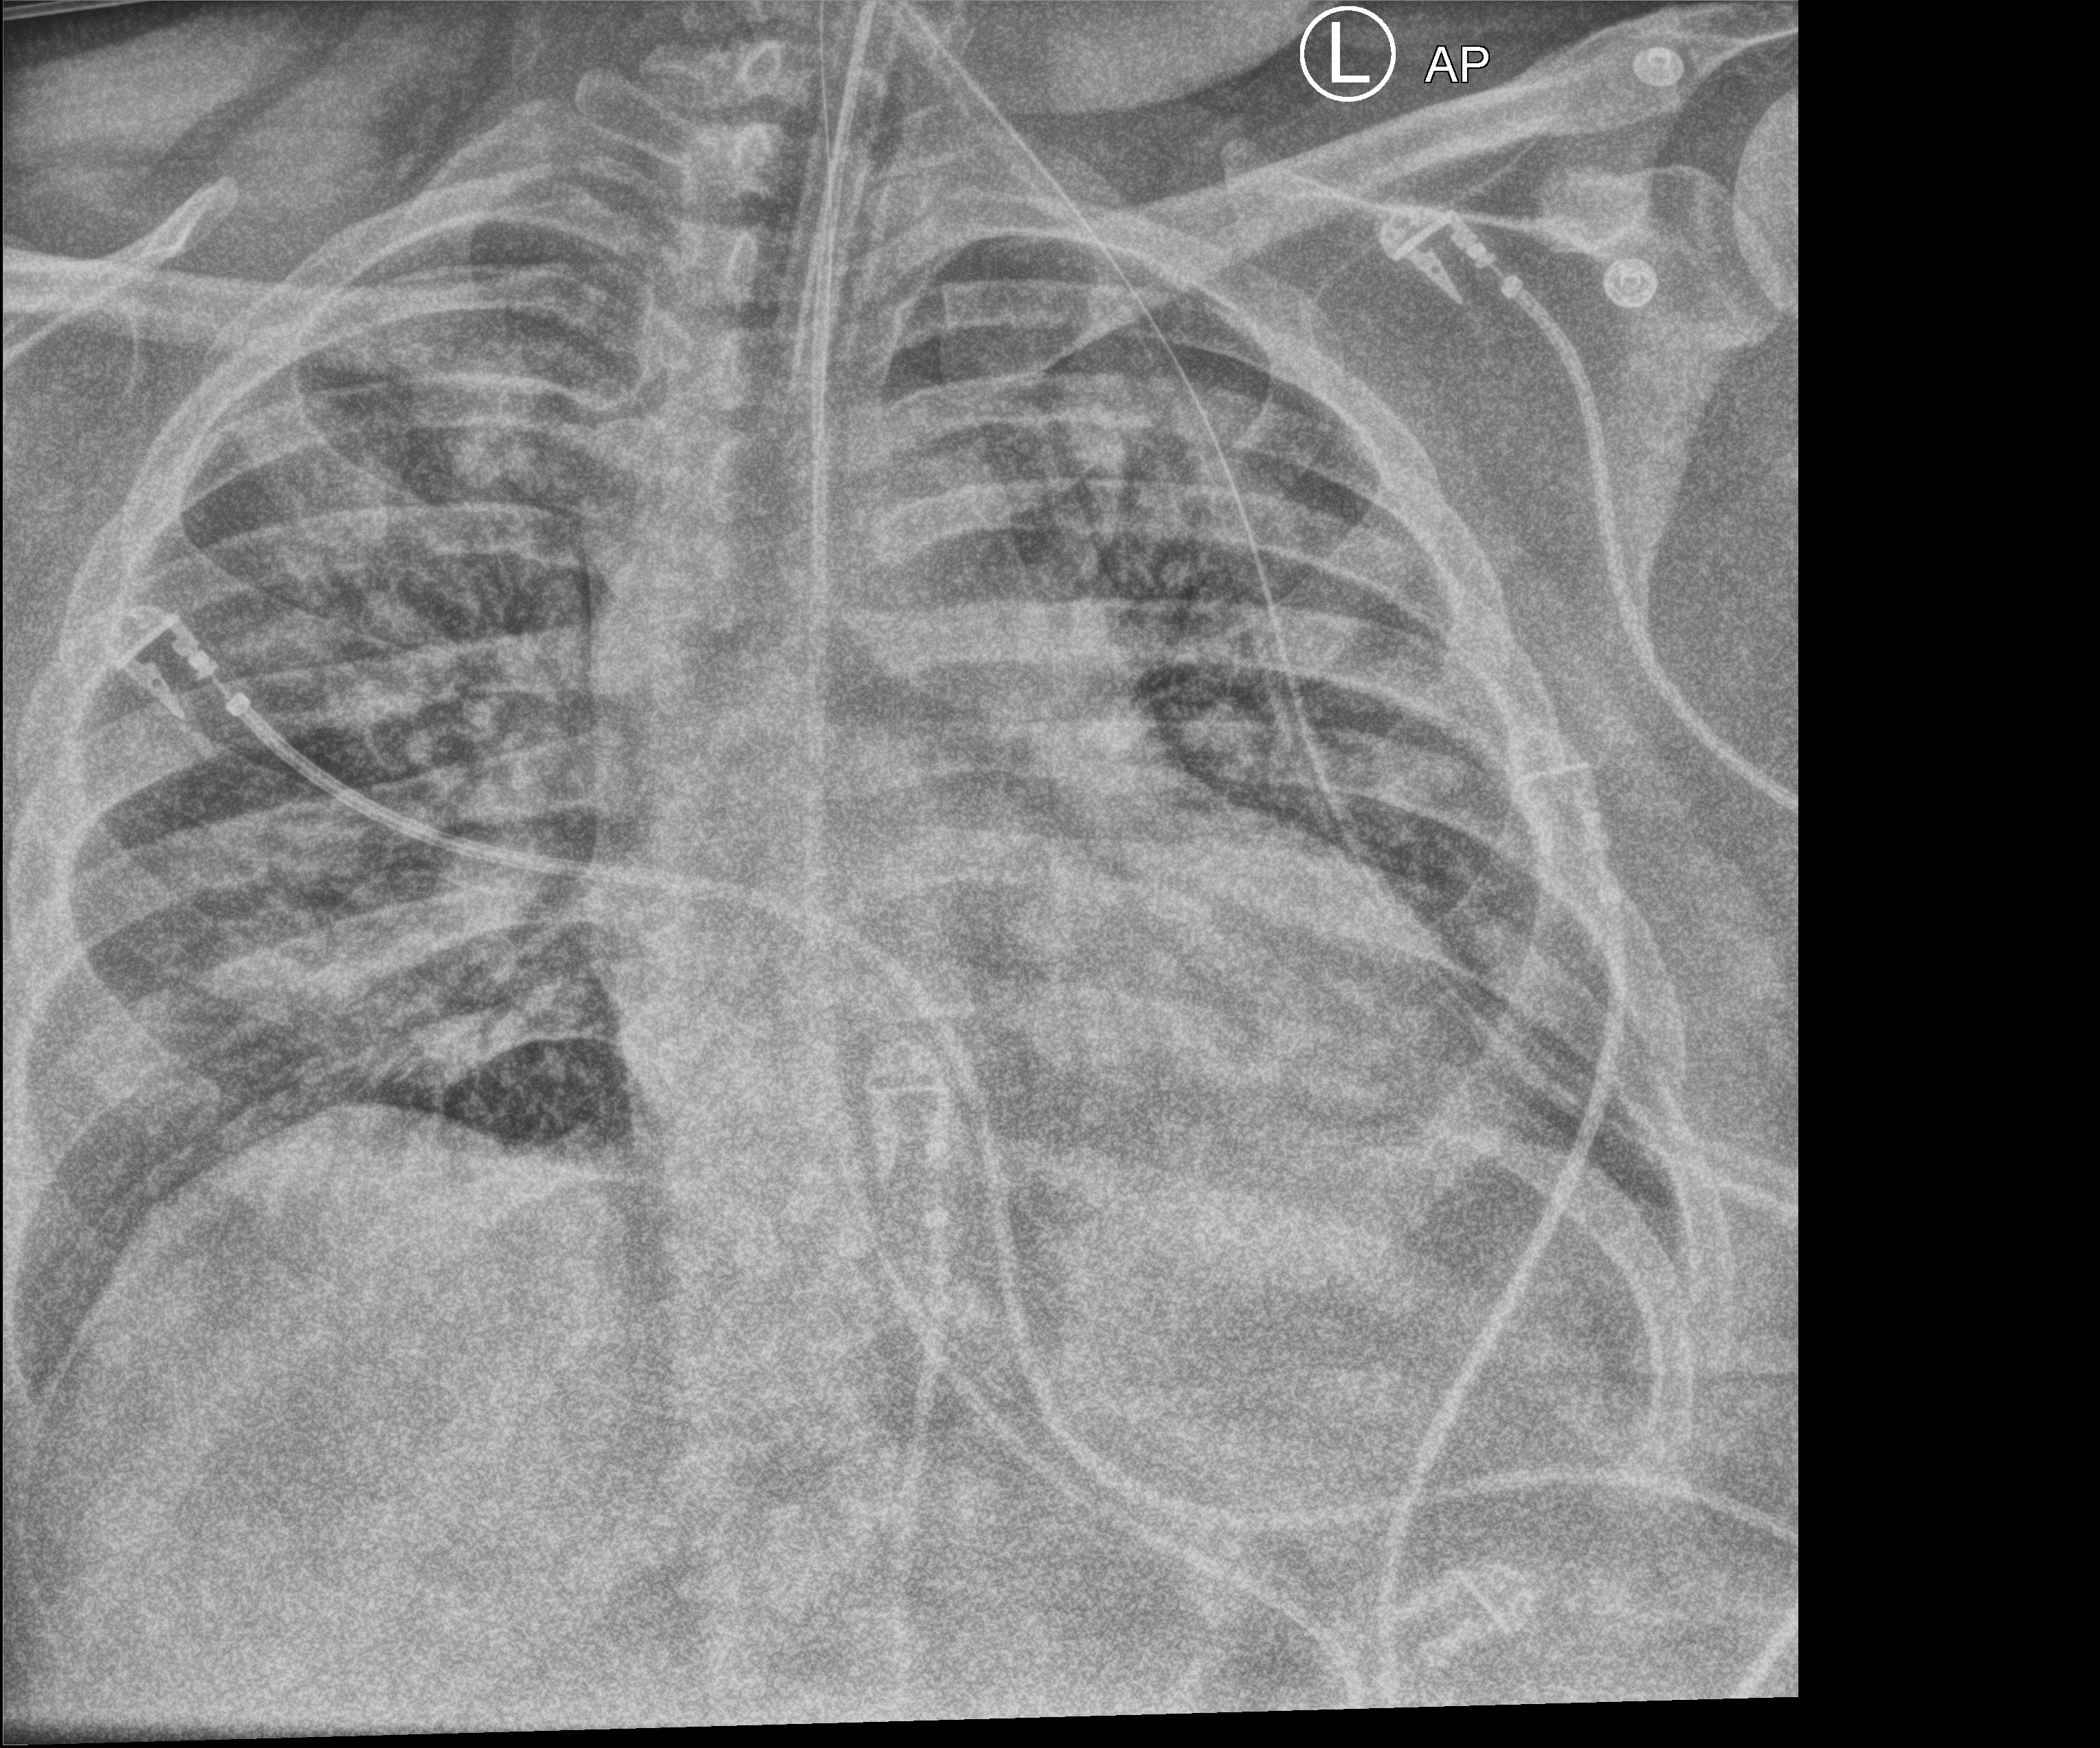
Bedside chest radiograph (computed radiography), anteroposterior (AP) projection. Adult patient hospitalised with COVID-19, age 18–59 years.
Admission-level facts for this patient (not findings on this image; timing relative to this image not recorded): admitted to intensive care during this hospital stay: yes; mechanically ventilated during this hospital stay: yes.